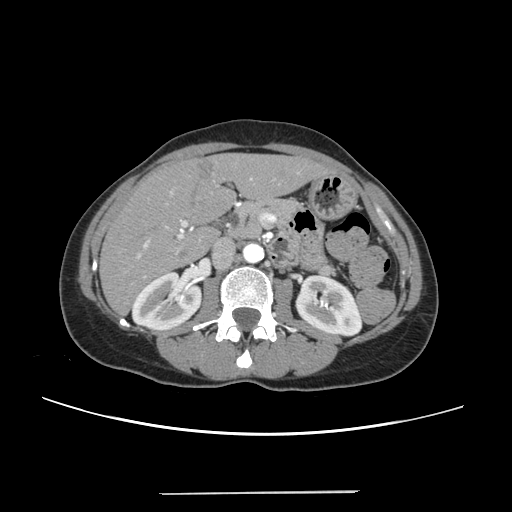
Contrast-enhanced abdominal CT, one axial slice. Position 117 of 240 along the scan axis. 120 kVp. Intravenous contrast given. Soft-tissue window (W 400 / L 40 HU). 1.25 mm slice thickness. 512 × 512 image matrix. Female patient, age 60 years. From the clinical record (not read from this slice): diagnosis: colorectal cancer liver metastases, imaged before liver resection.
Outlined on this slice (outlined manually by an expert reader):
- liver: bounding box <101,153,328,313> (left, top, right, bottom; pixels)
- planned liver remnant (the part of the liver to remain after resection): <101,155,328,312>
- portal vein (with intrahepatic branches): <138,178,254,277>
- liver metastasis: <197,160,214,181>